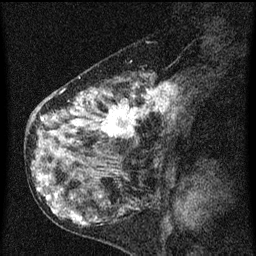
Breast MRI (dynamic contrast-enhanced), one sagittal slice. Position 28 of 60 along the scan axis. Dynamic contrast-enhanced series, image 2 of 3 at this slice position (ordered by acquisition). 1.5 T. TE 4.2 ms, TR 8 ms. 2 mm slice thickness. 256 × 256 image matrix, field of view 180 × 180 mm. Patient: female, 55 years.
Outlined on this slice (semi-automatically segmented with operator editing):
- analysis volume of interest (the breast-tissue region the enhancement analysis was run in; not a lesion): bounding box [x1, y1, x2, y2] px = [42, 72, 185, 155]
- tumour enhancement mask (voxels above the 70 % enhancement threshold inside the analysis volume of interest): [76, 82, 177, 139]